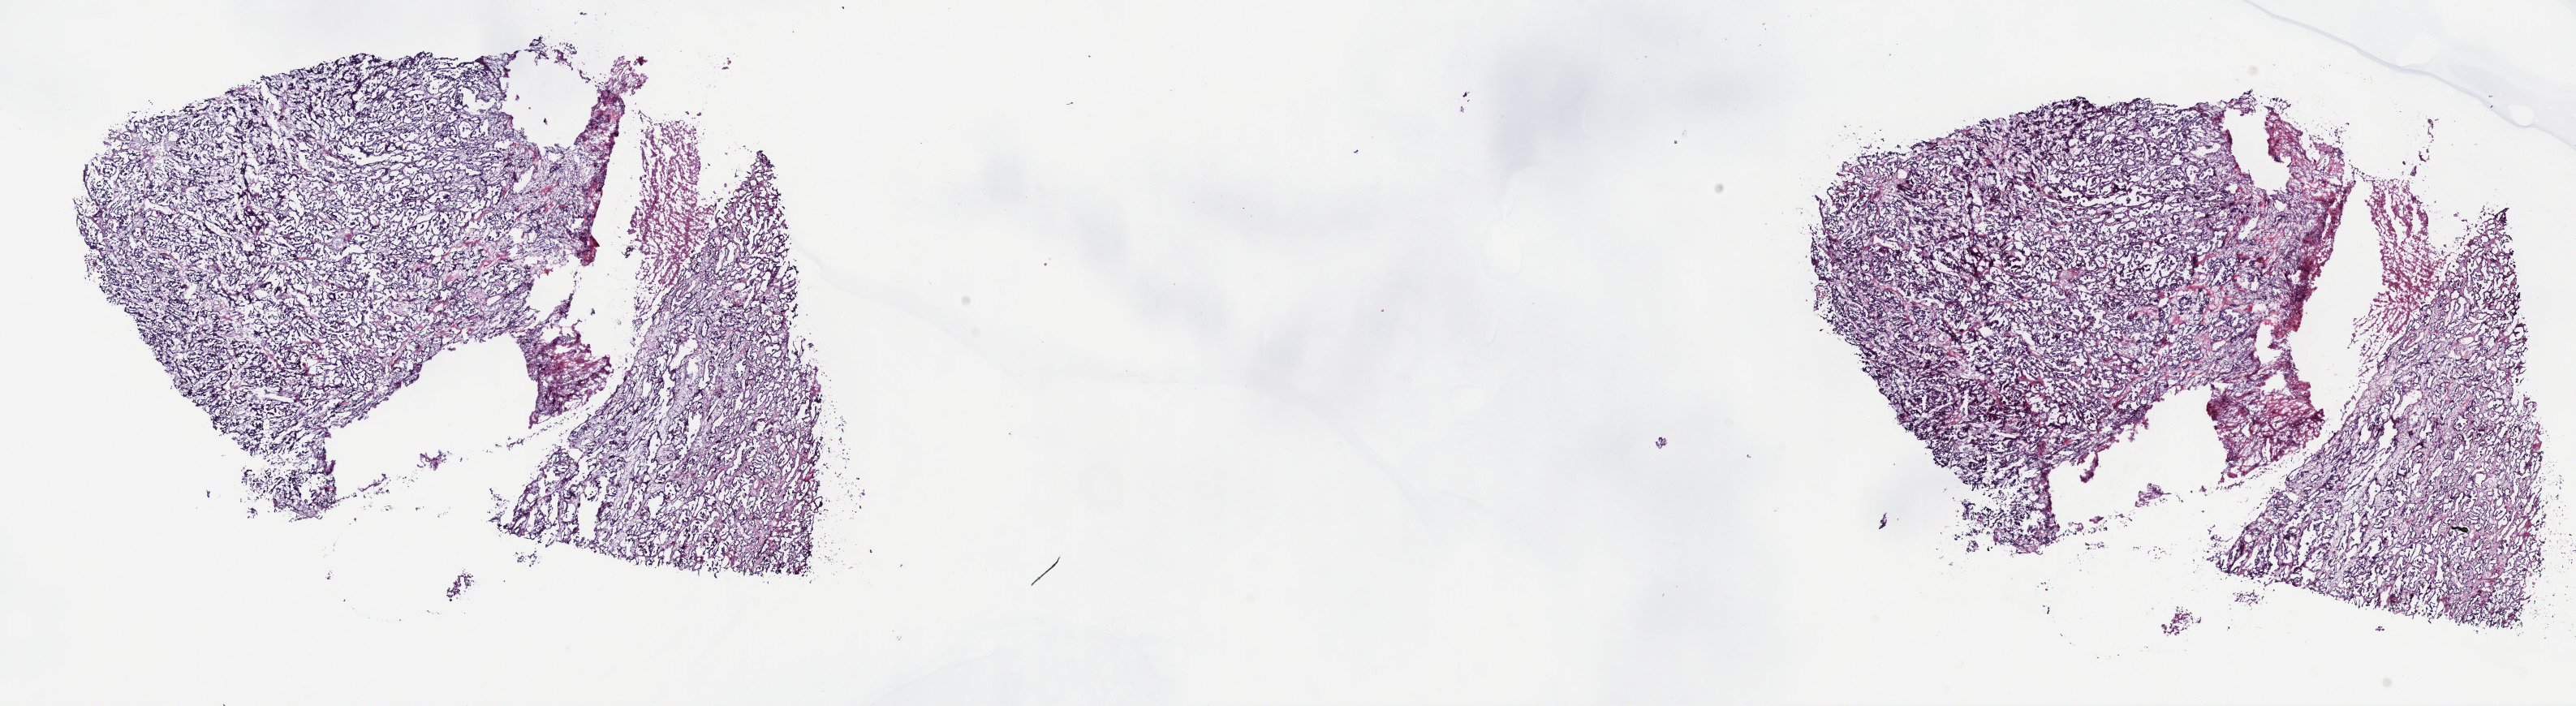
Digitized H&E-stained tissue section (whole slide) — shown as a low-resolution overview of the whole scanned area (about 25.7 x 7.0 mm); frozen section; primary tumour sample from the kidney. Patient: male, age at initial diagnosis 85 years. Slide review estimates, as recorded: tumour cells 75%, tumour nuclei 75%, normal cells 0%, stromal cells 21%, necrosis 4%. Infiltration values recorded for this section: lymphocyte infiltration 2%, monocyte infiltration 4%, neutrophil infiltration 2%.
AJCC pathologic stage: III (7th edition). Diagnosis: Papillary adenocarcinoma, NOS. Lymph nodes positive (case pathology): 1 of 21 examined. TNM: T3b N0 MX.